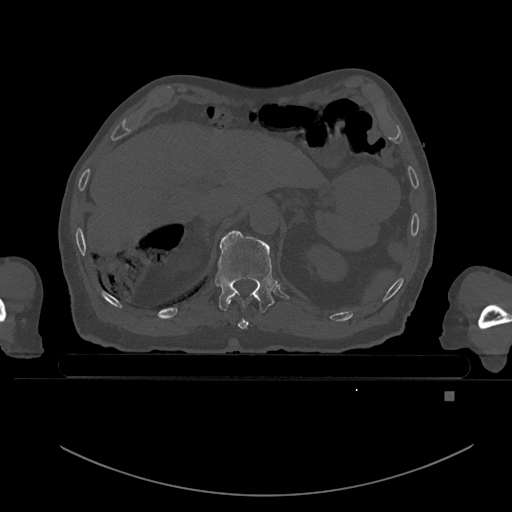
CT including the spine, one axial slice. Slice 43 of 969 in the series (ordered by position). Bone window (W 1800 / L 400 HU). 0.5 mm slice thickness. 512 × 512 image matrix, field of view 456 × 456 mm. Patient: male, 82 years. Case-level facts recorded for this patient, not image findings: primary cancer: prostate.
Outlined on this slice (semi-automatic segmentation, software-assisted and operator-edited):
- T10 vertebra: bounding box [x1, y1, x2, y2] px = [238, 319, 248, 330]
- T11 vertebra: [215, 230, 278, 313]